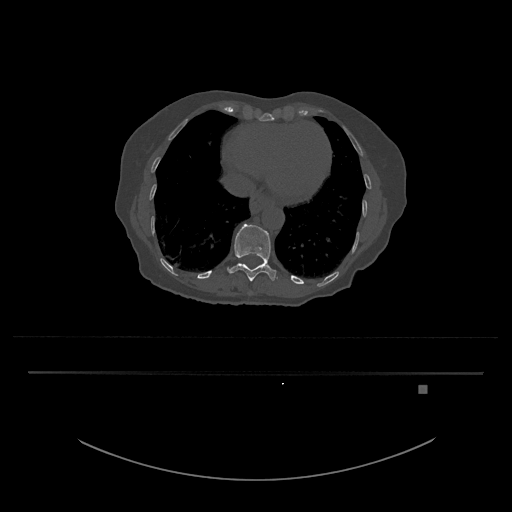
CT including the spine, one axial slice; position 665 of 797 along the scan axis; reconstruction kernel Br40s/3; bone window (W 1800 / L 400 HU); 0.5 mm slice thickness; 512 × 512 image matrix, field of view 500 × 500 mm. Patient: female, 57 years. Case-level facts recorded for this patient, not image findings: primary cancer: cervical.
Annotated regions visible in this slice (semi-automatic segmentation, software-assisted and operator-edited):
- T11 vertebra: box from (x=227, y=224) to (x=277, y=281) px